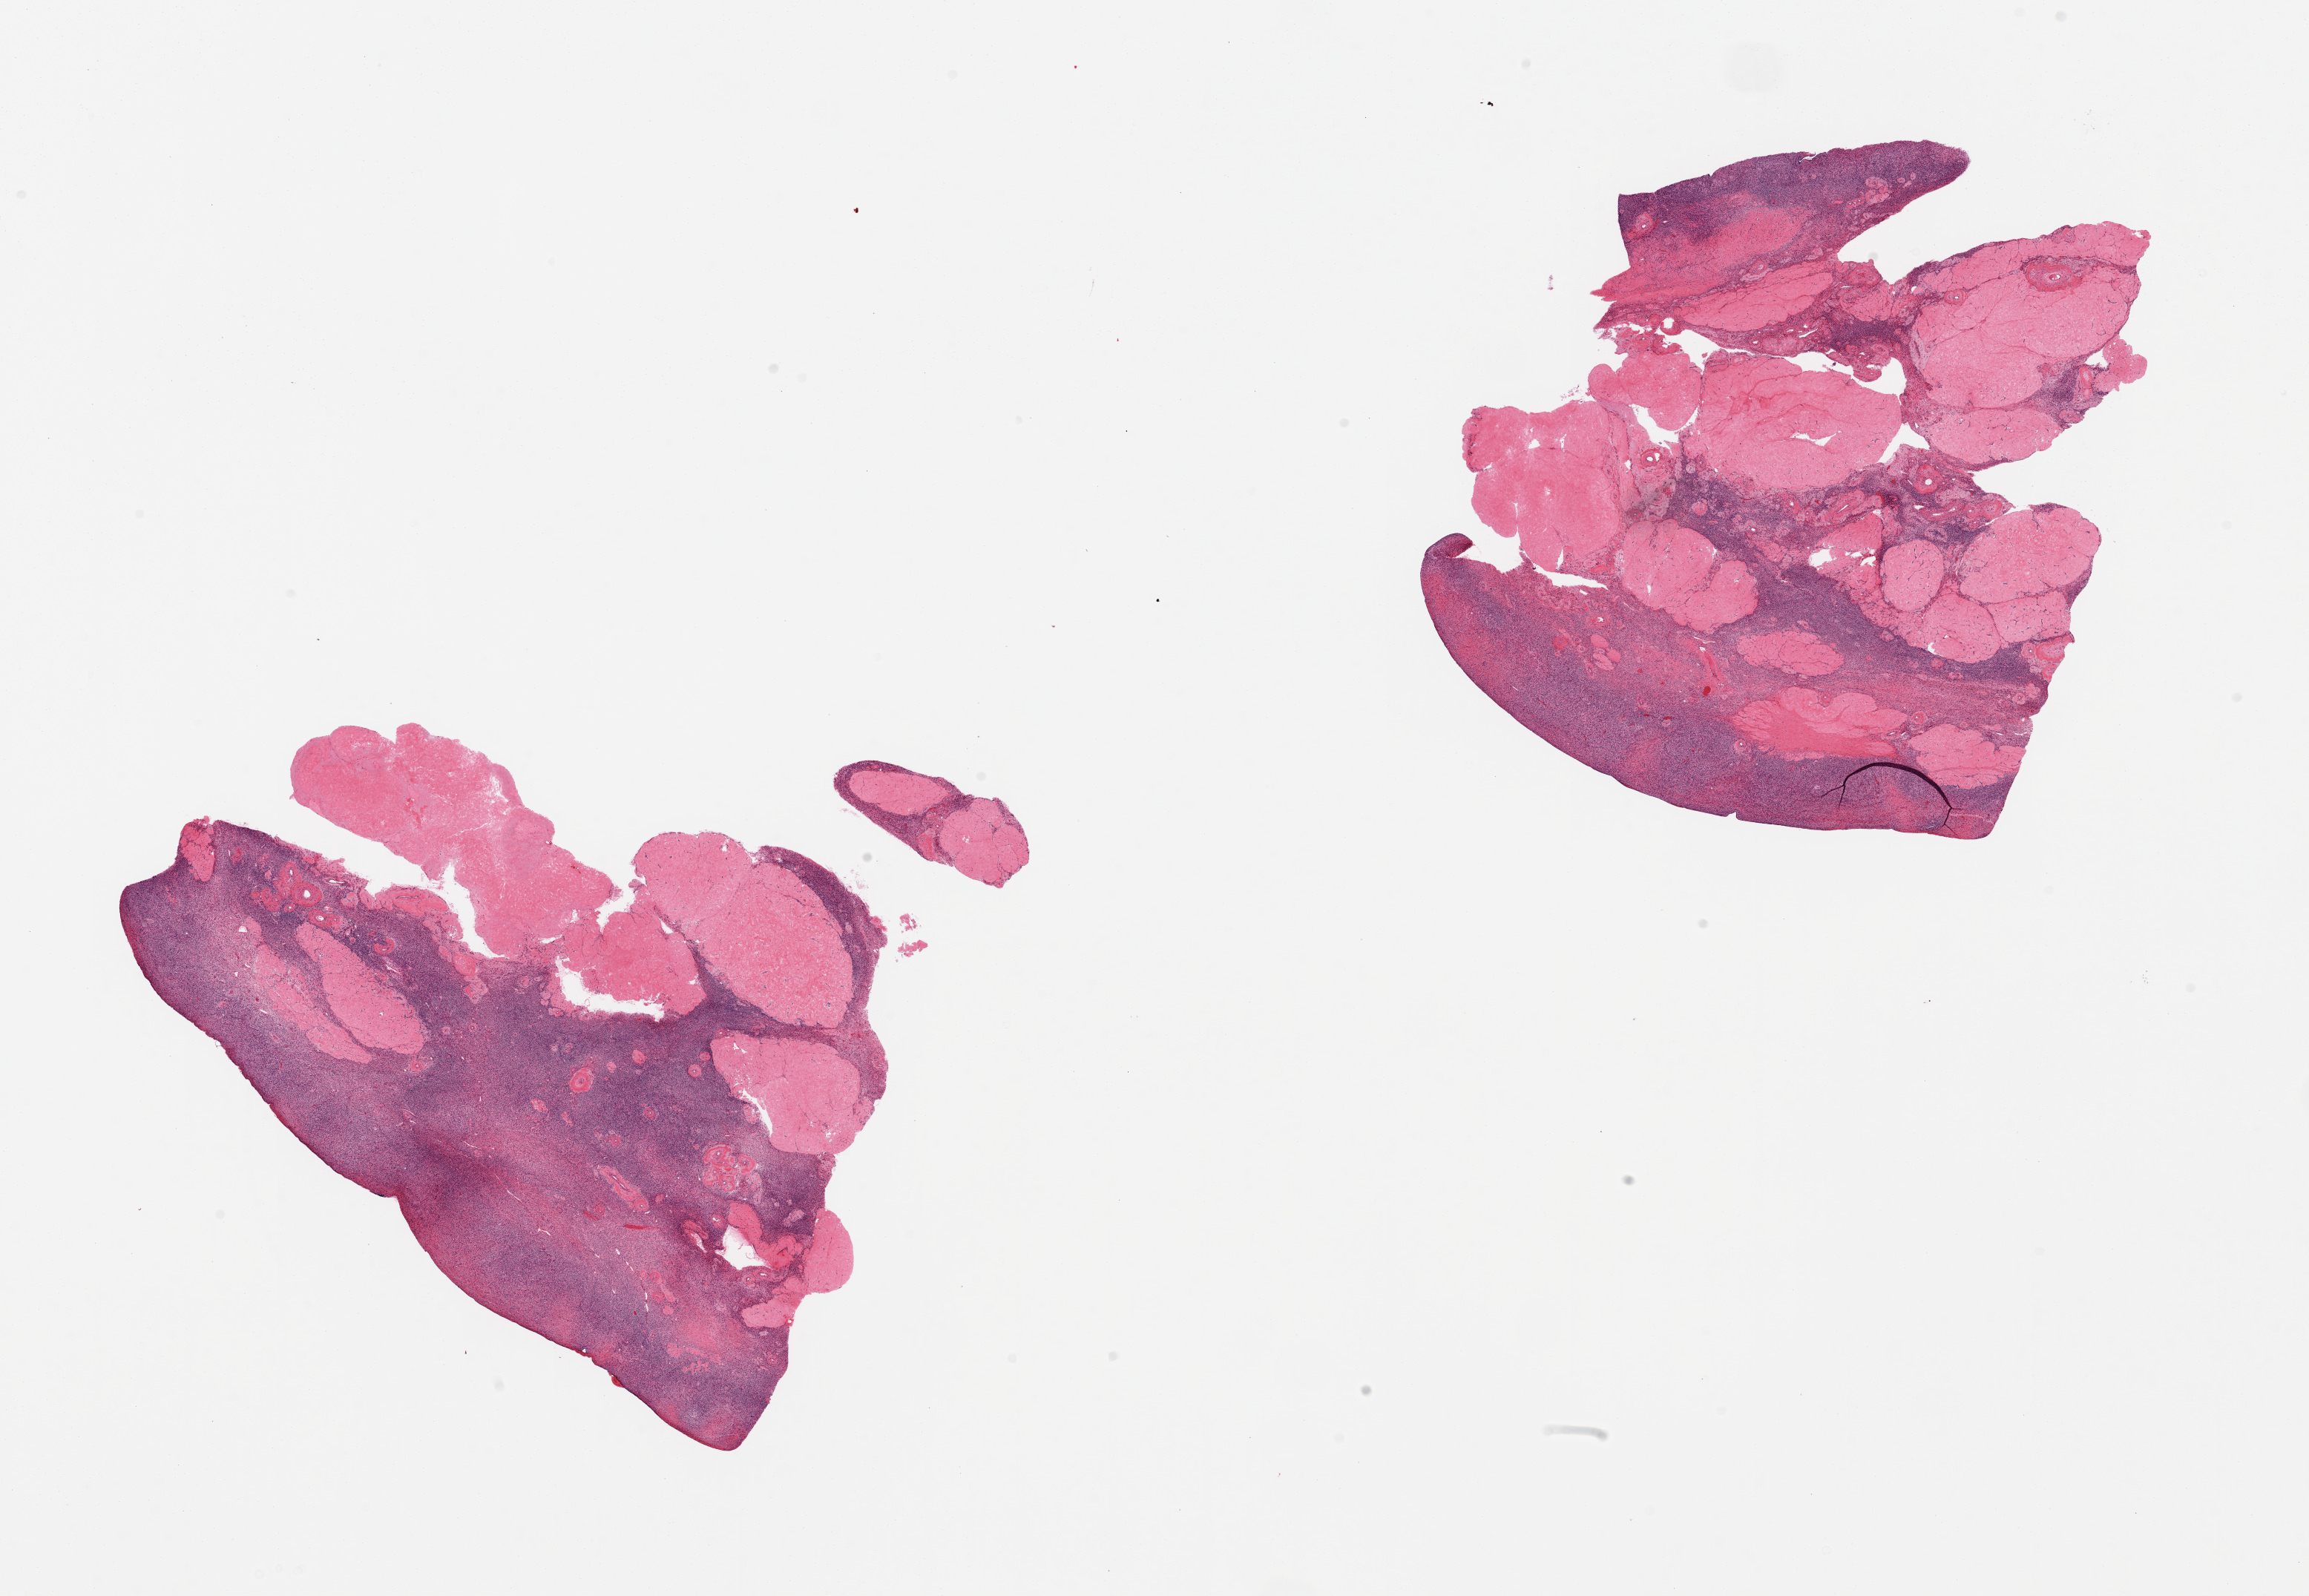
Haematoxylin and eosin whole-slide image, whole scanned area (about 24.6 x 17.0 mm) shown as a low-resolution overview. PAXgene-fixed paraffin-embedded (PFPE) section. Sampled site (target tissue): ovary. Donor tissue sample. Donor sex: female.
Review note (as recorded): 2 pieces, several corpora albicantia.